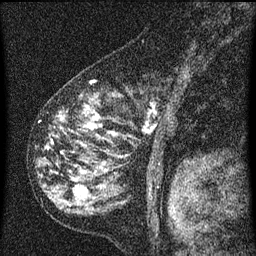
Breast MRI (dynamic contrast-enhanced), one sagittal slice. Slice 39 of 60 in the series (ordered by position). Dynamic contrast-enhanced series, image 2 of 3 at this slice position (ordered by acquisition). 1.5 T. TE 4.2 ms, TR 8 ms. 2 mm slice thickness. 256 × 256 image matrix. Patient: female, 55 years.
Structures marked on this image (semi-automatic segmentation, software-assisted and operator-edited):
- analysis volume of interest (the breast-tissue region the enhancement analysis was run in; not a lesion): bounding box <44,74,185,155> (left, top, right, bottom; pixels)
- tumour enhancement mask (voxels above the 70 % enhancement threshold inside the analysis volume of interest): <61,116,116,135>